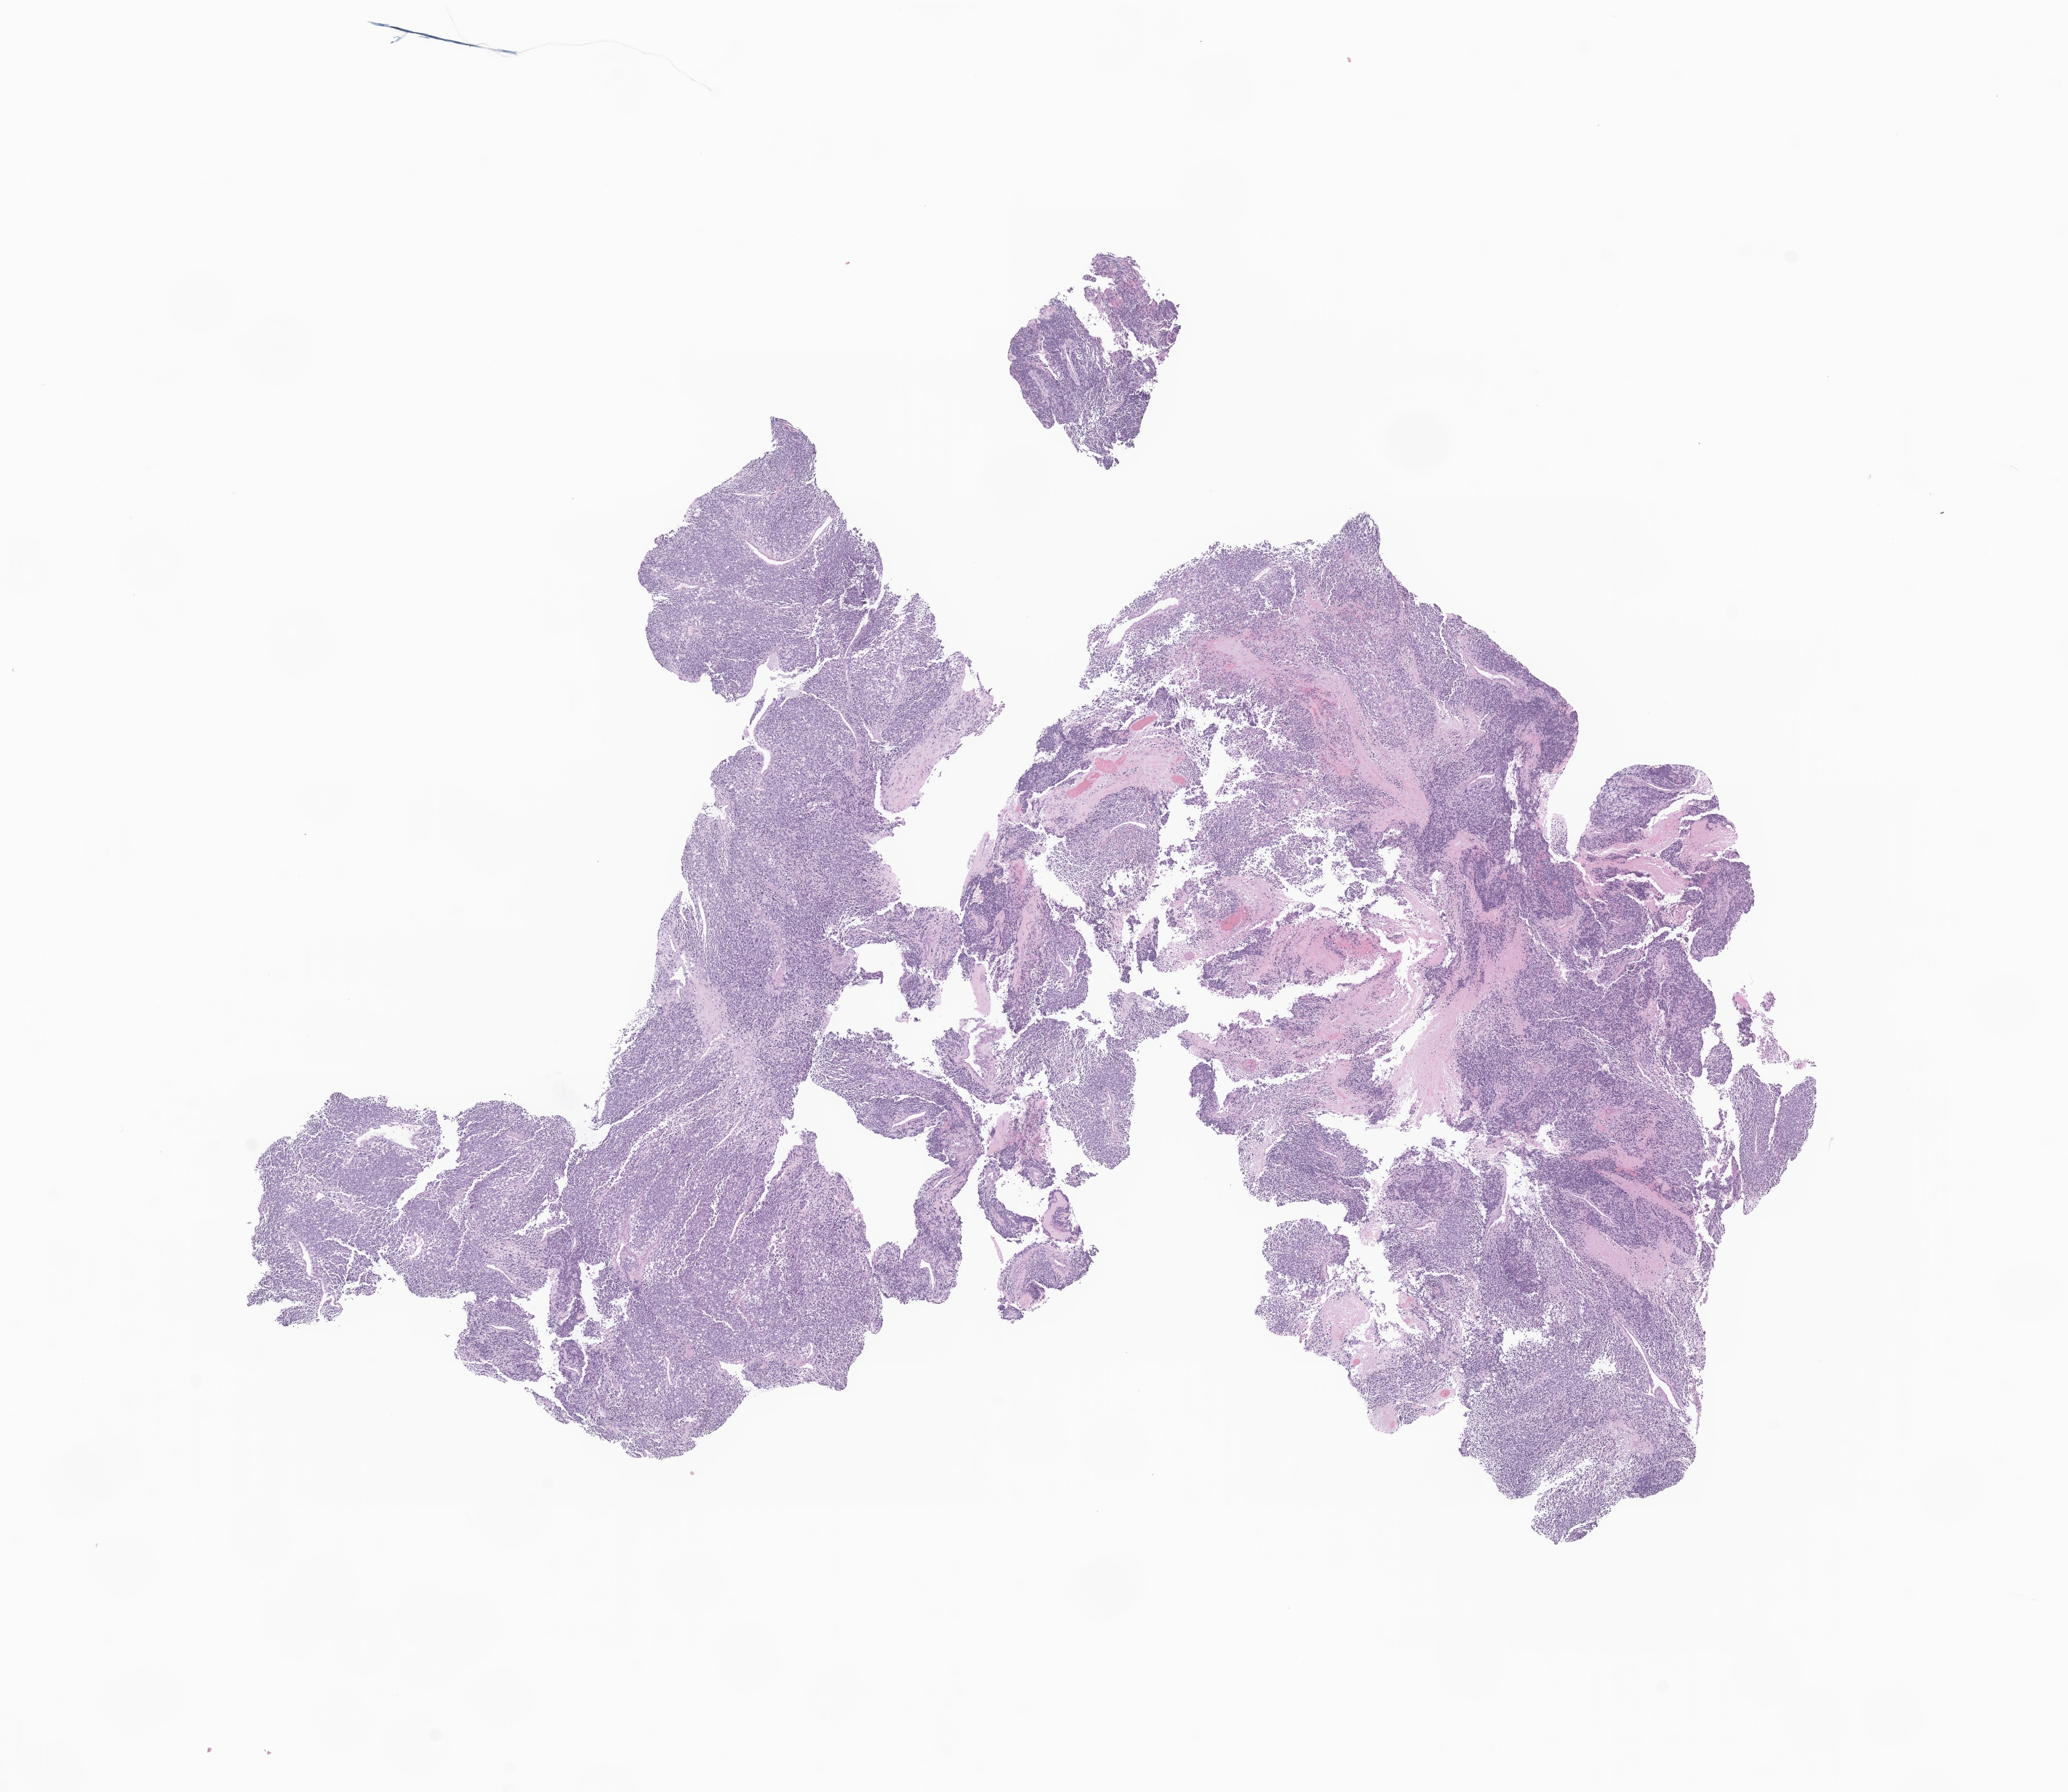
Digitized H&E-stained section of tumor tissue from the buccal mucosa — low-resolution overview of the scanned area, about 15.3 x 13.3 mm; formalin-fixed paraffin-embedded section. Male patient, age 96 months (8 years).
Diagnosis (ICD-O-3 morphology term): Alveolar rhabdomyosarcoma.